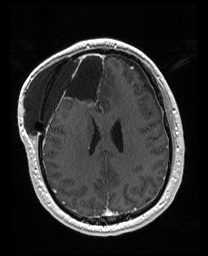
Brain MRI from a brain-tumour surgery series, one axial slice. Slice 70 of 176 in the series (ordered by position). T1-weighted post-contrast. 1 mm slice thickness. 208 × 256 image matrix. From the clinical record (not read from this slice): histopathology: Astrocytoma; WHO grade: 4; IDH mutation: yes; tumour location: Right Orbitofrontal Anterior Temporal Insular.
Annotated regions visible in this slice (manually delineated by an expert):
- previous resection cavity: box from (x=56, y=52) to (x=106, y=111) px